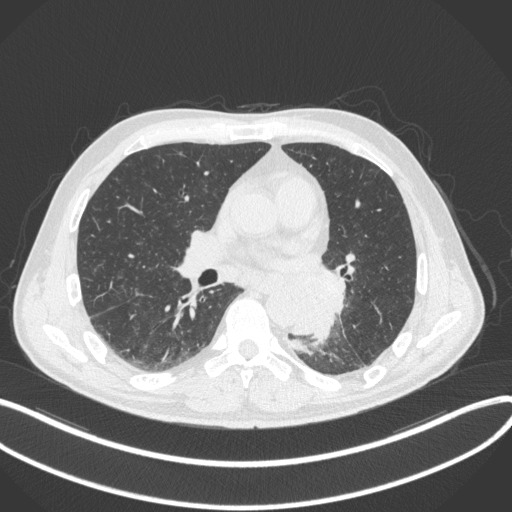
Chest CT, one axial slice. Slice 171 of 328 in the series (ordered by position). 120 kVp. Lung window (W 1500 / L -600 HU). 512 × 512 image matrix, field of view 400 × 400 mm. Patient: male, 59 years. From the clinical record (not read from this slice): clinical TNM (as recorded): T2a N2 M0.
Structures marked on this image (bounding box drawn by a radiologist):
- lung tumour (recorded histology: squamous cell carcinoma): bounding box [x1, y1, x2, y2] px = [285, 263, 346, 344]